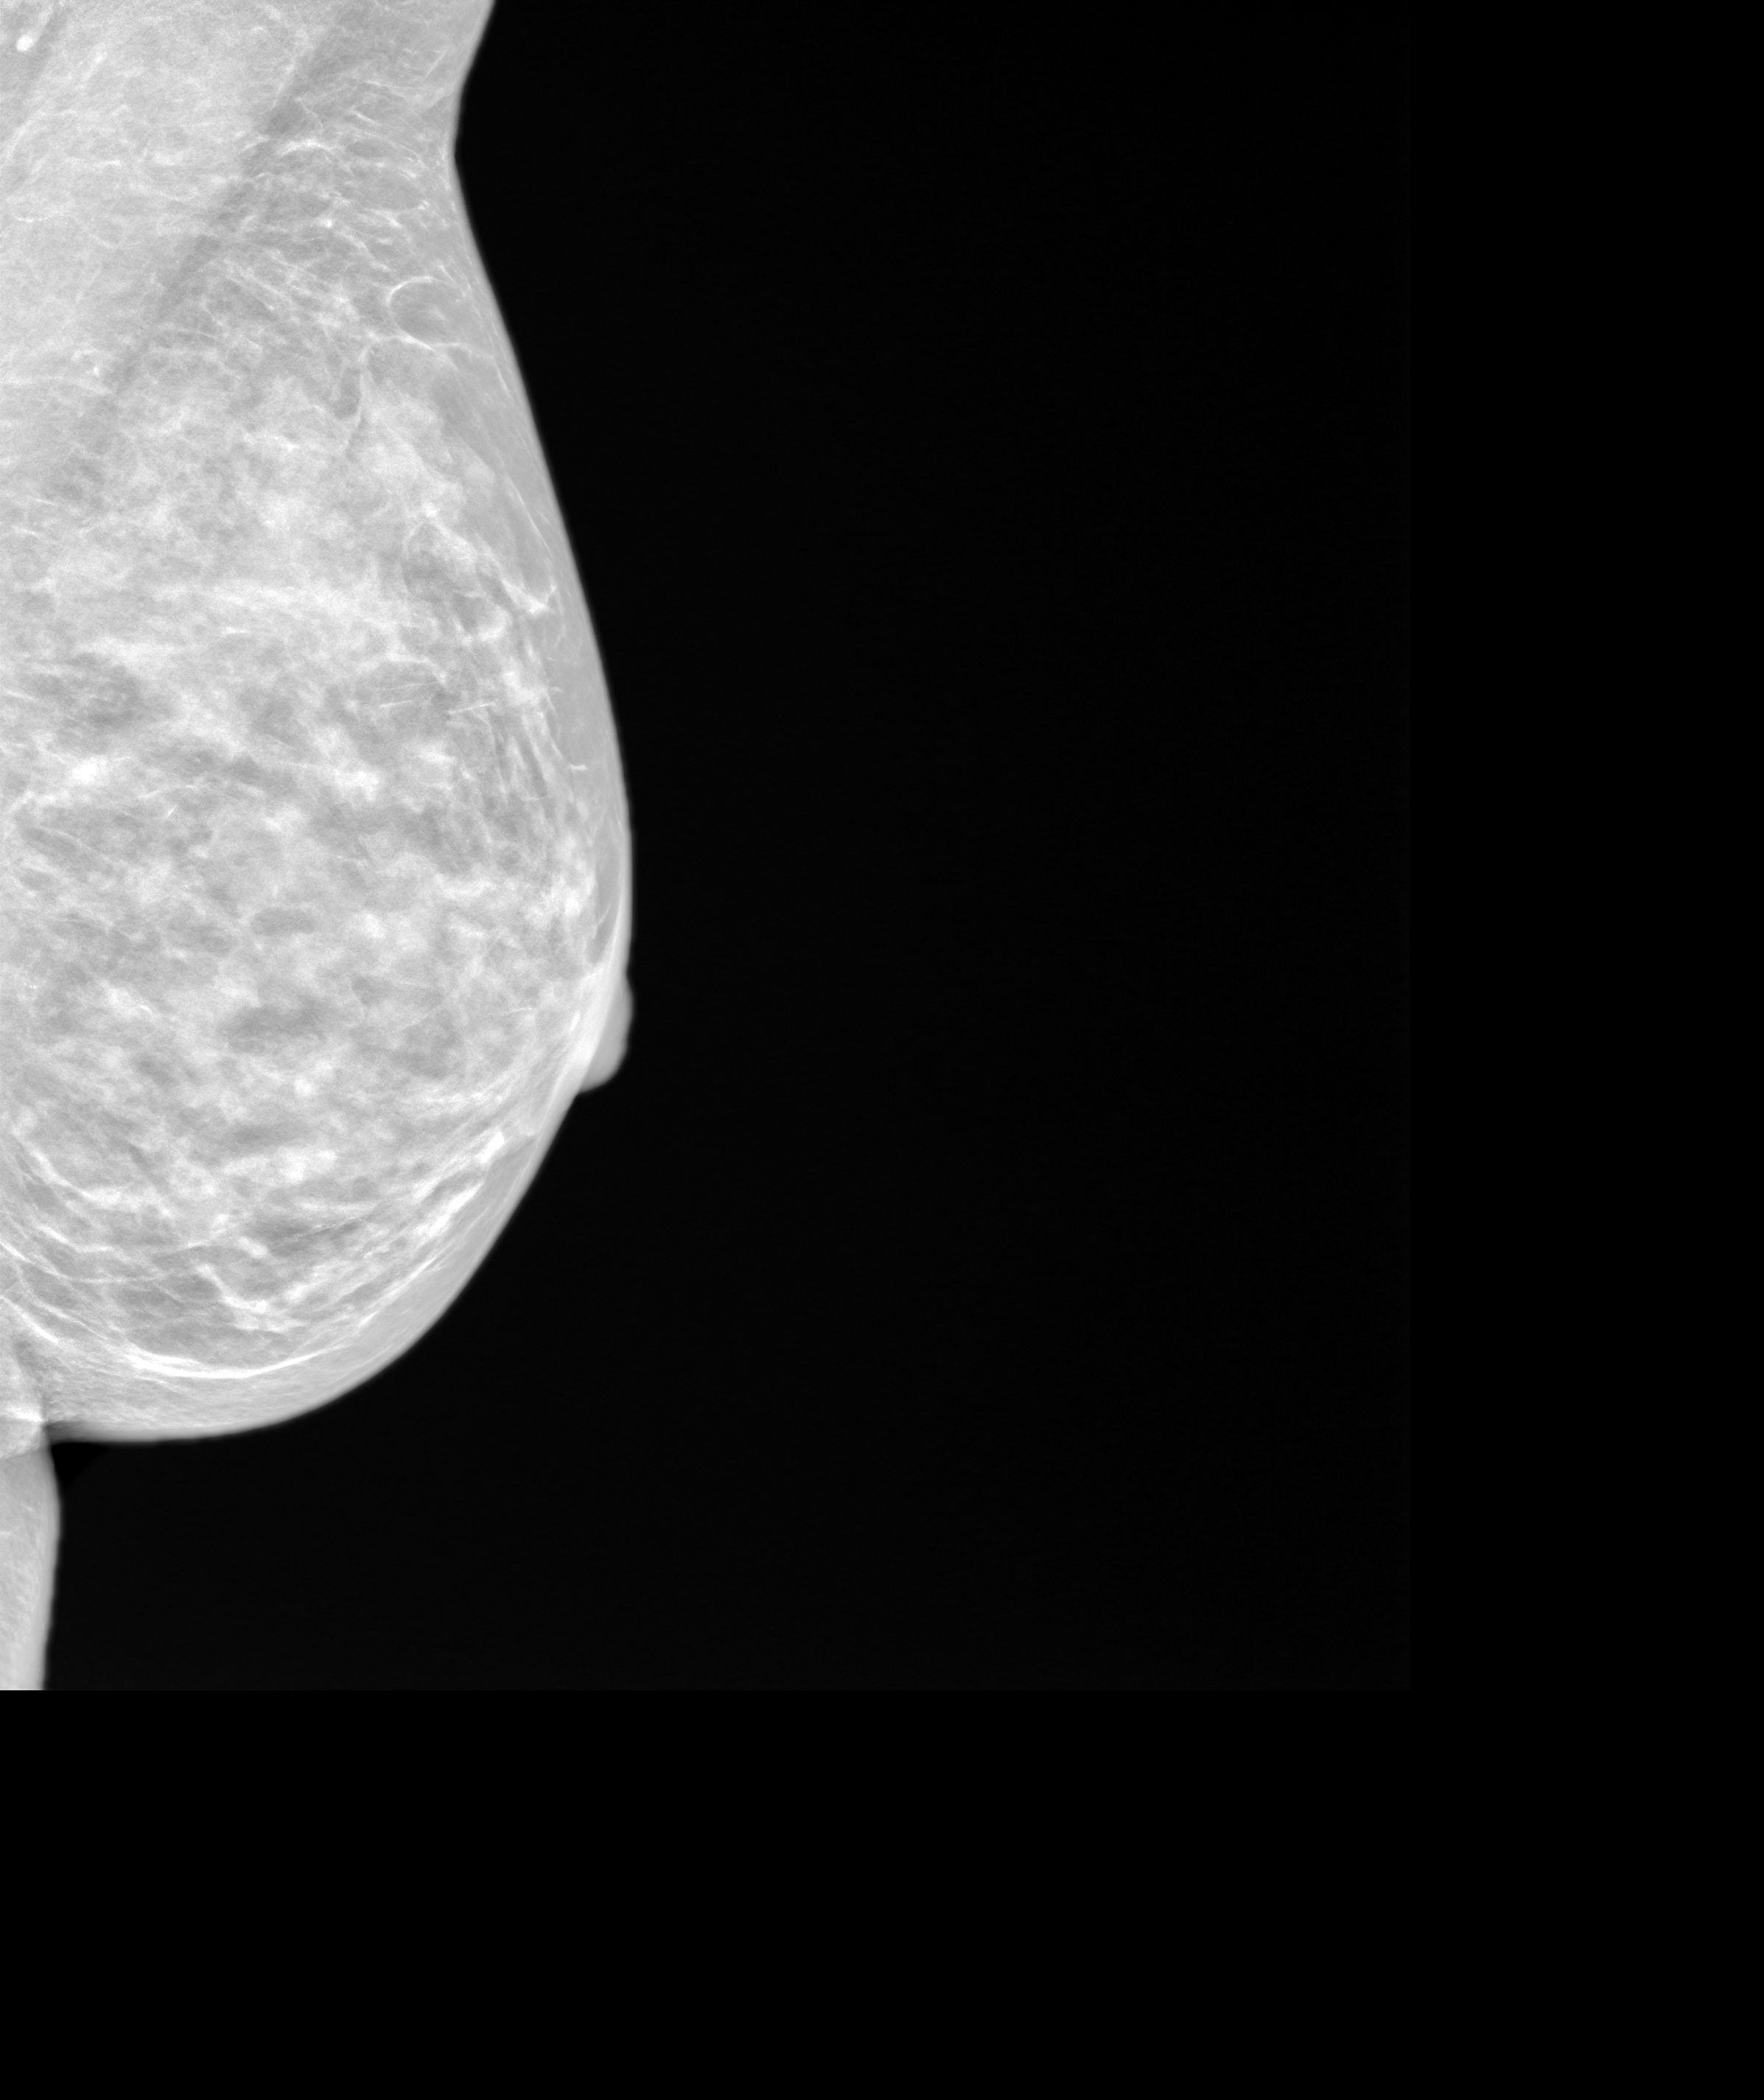
Annual screening mammography examination. Patient aged 74 years (female).
Image type: synthesized 2-D view from tomosynthesis. Breast: left. Projection: MLO view.